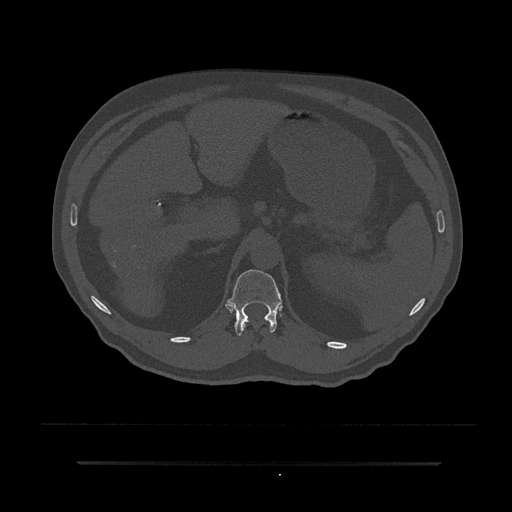
CT including the spine, one axial slice. Position 224 of 797 along the scan axis. Bone window (W 1800 / L 400 HU). 512 × 512 image matrix, field of view 464 × 464 mm. Male patient, age 59 years. From the clinical record (not read from this slice): primary cancer: bile ducts; vertebrae with lytic lesions (as recorded): T10.
Structures marked on this image (semi-automatically segmented with operator editing):
- T12 vertebra: box from (x=228, y=269) to (x=282, y=336) px